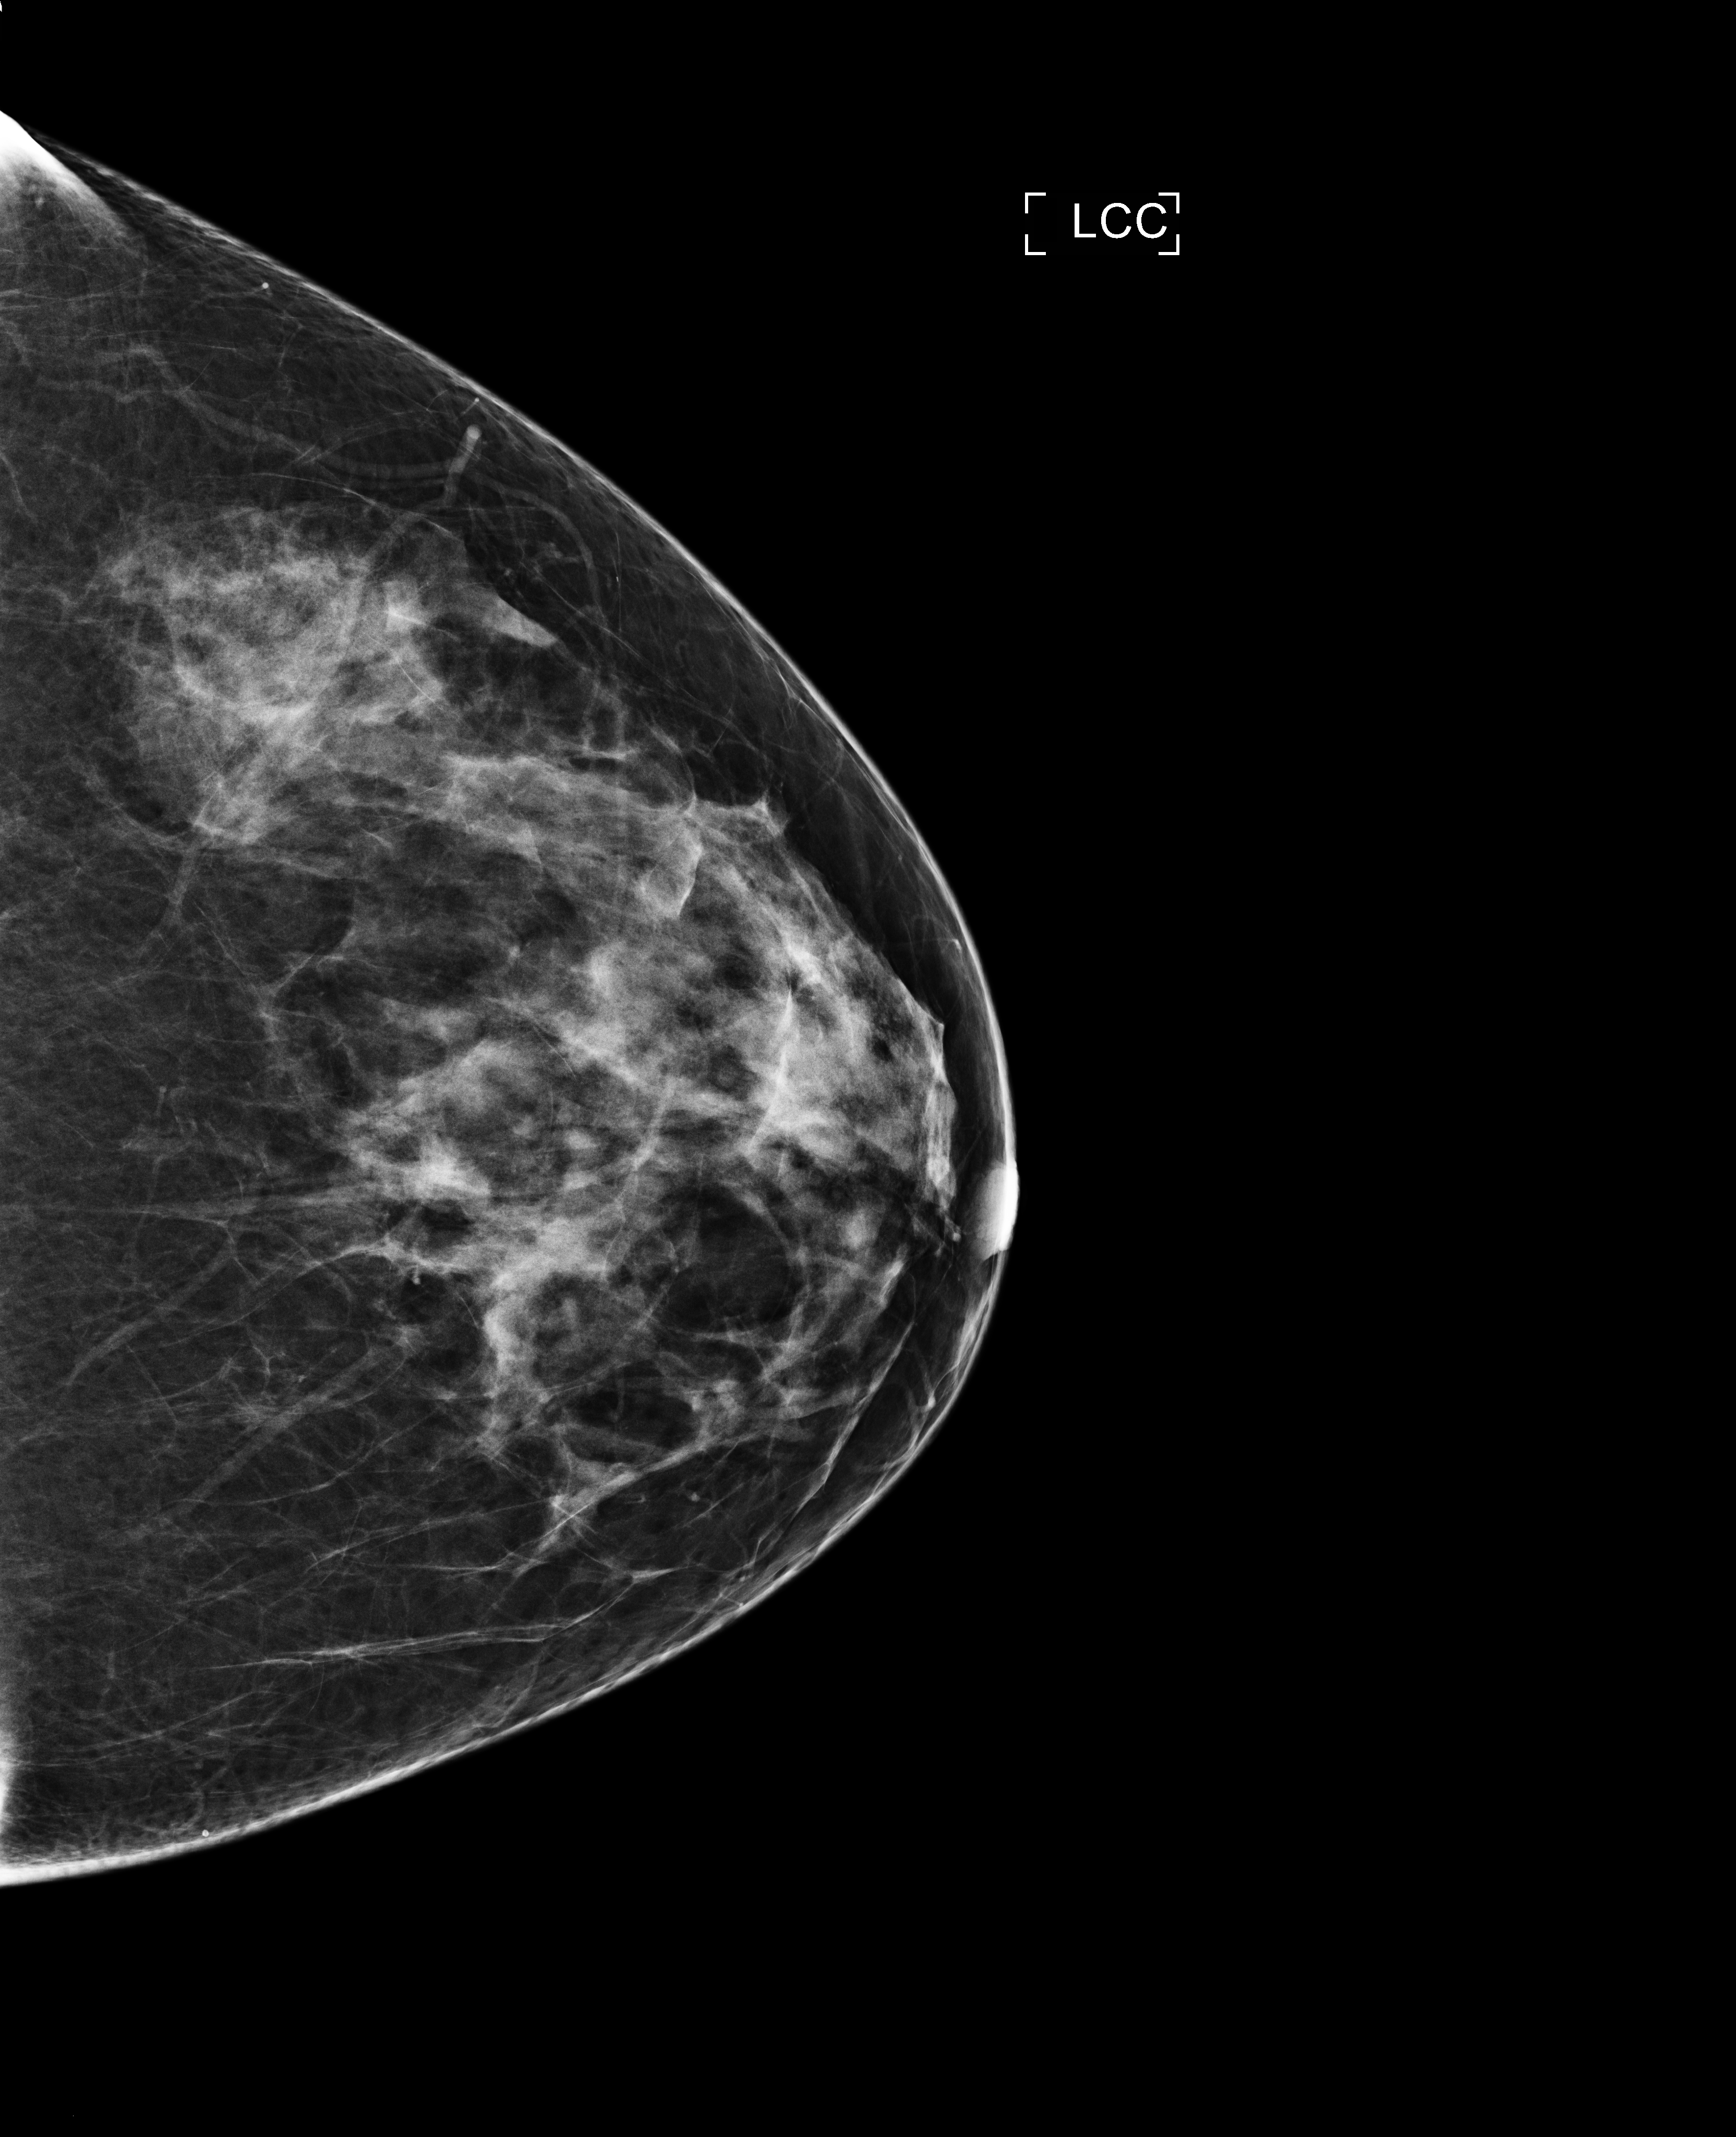
Full-field digital mammogram (FFDM), left breast, CC view, annual screening mammography examination, system: Selenia Dimensions. Patient: female, 45 years.
- breast density at the screening exam (both breasts): heterogeneously dense (BI-RADS density category c)
- final BI-RADS category for the screening round (tomosynthesis exam, both breasts): category 1
- recall: no recall after this screen